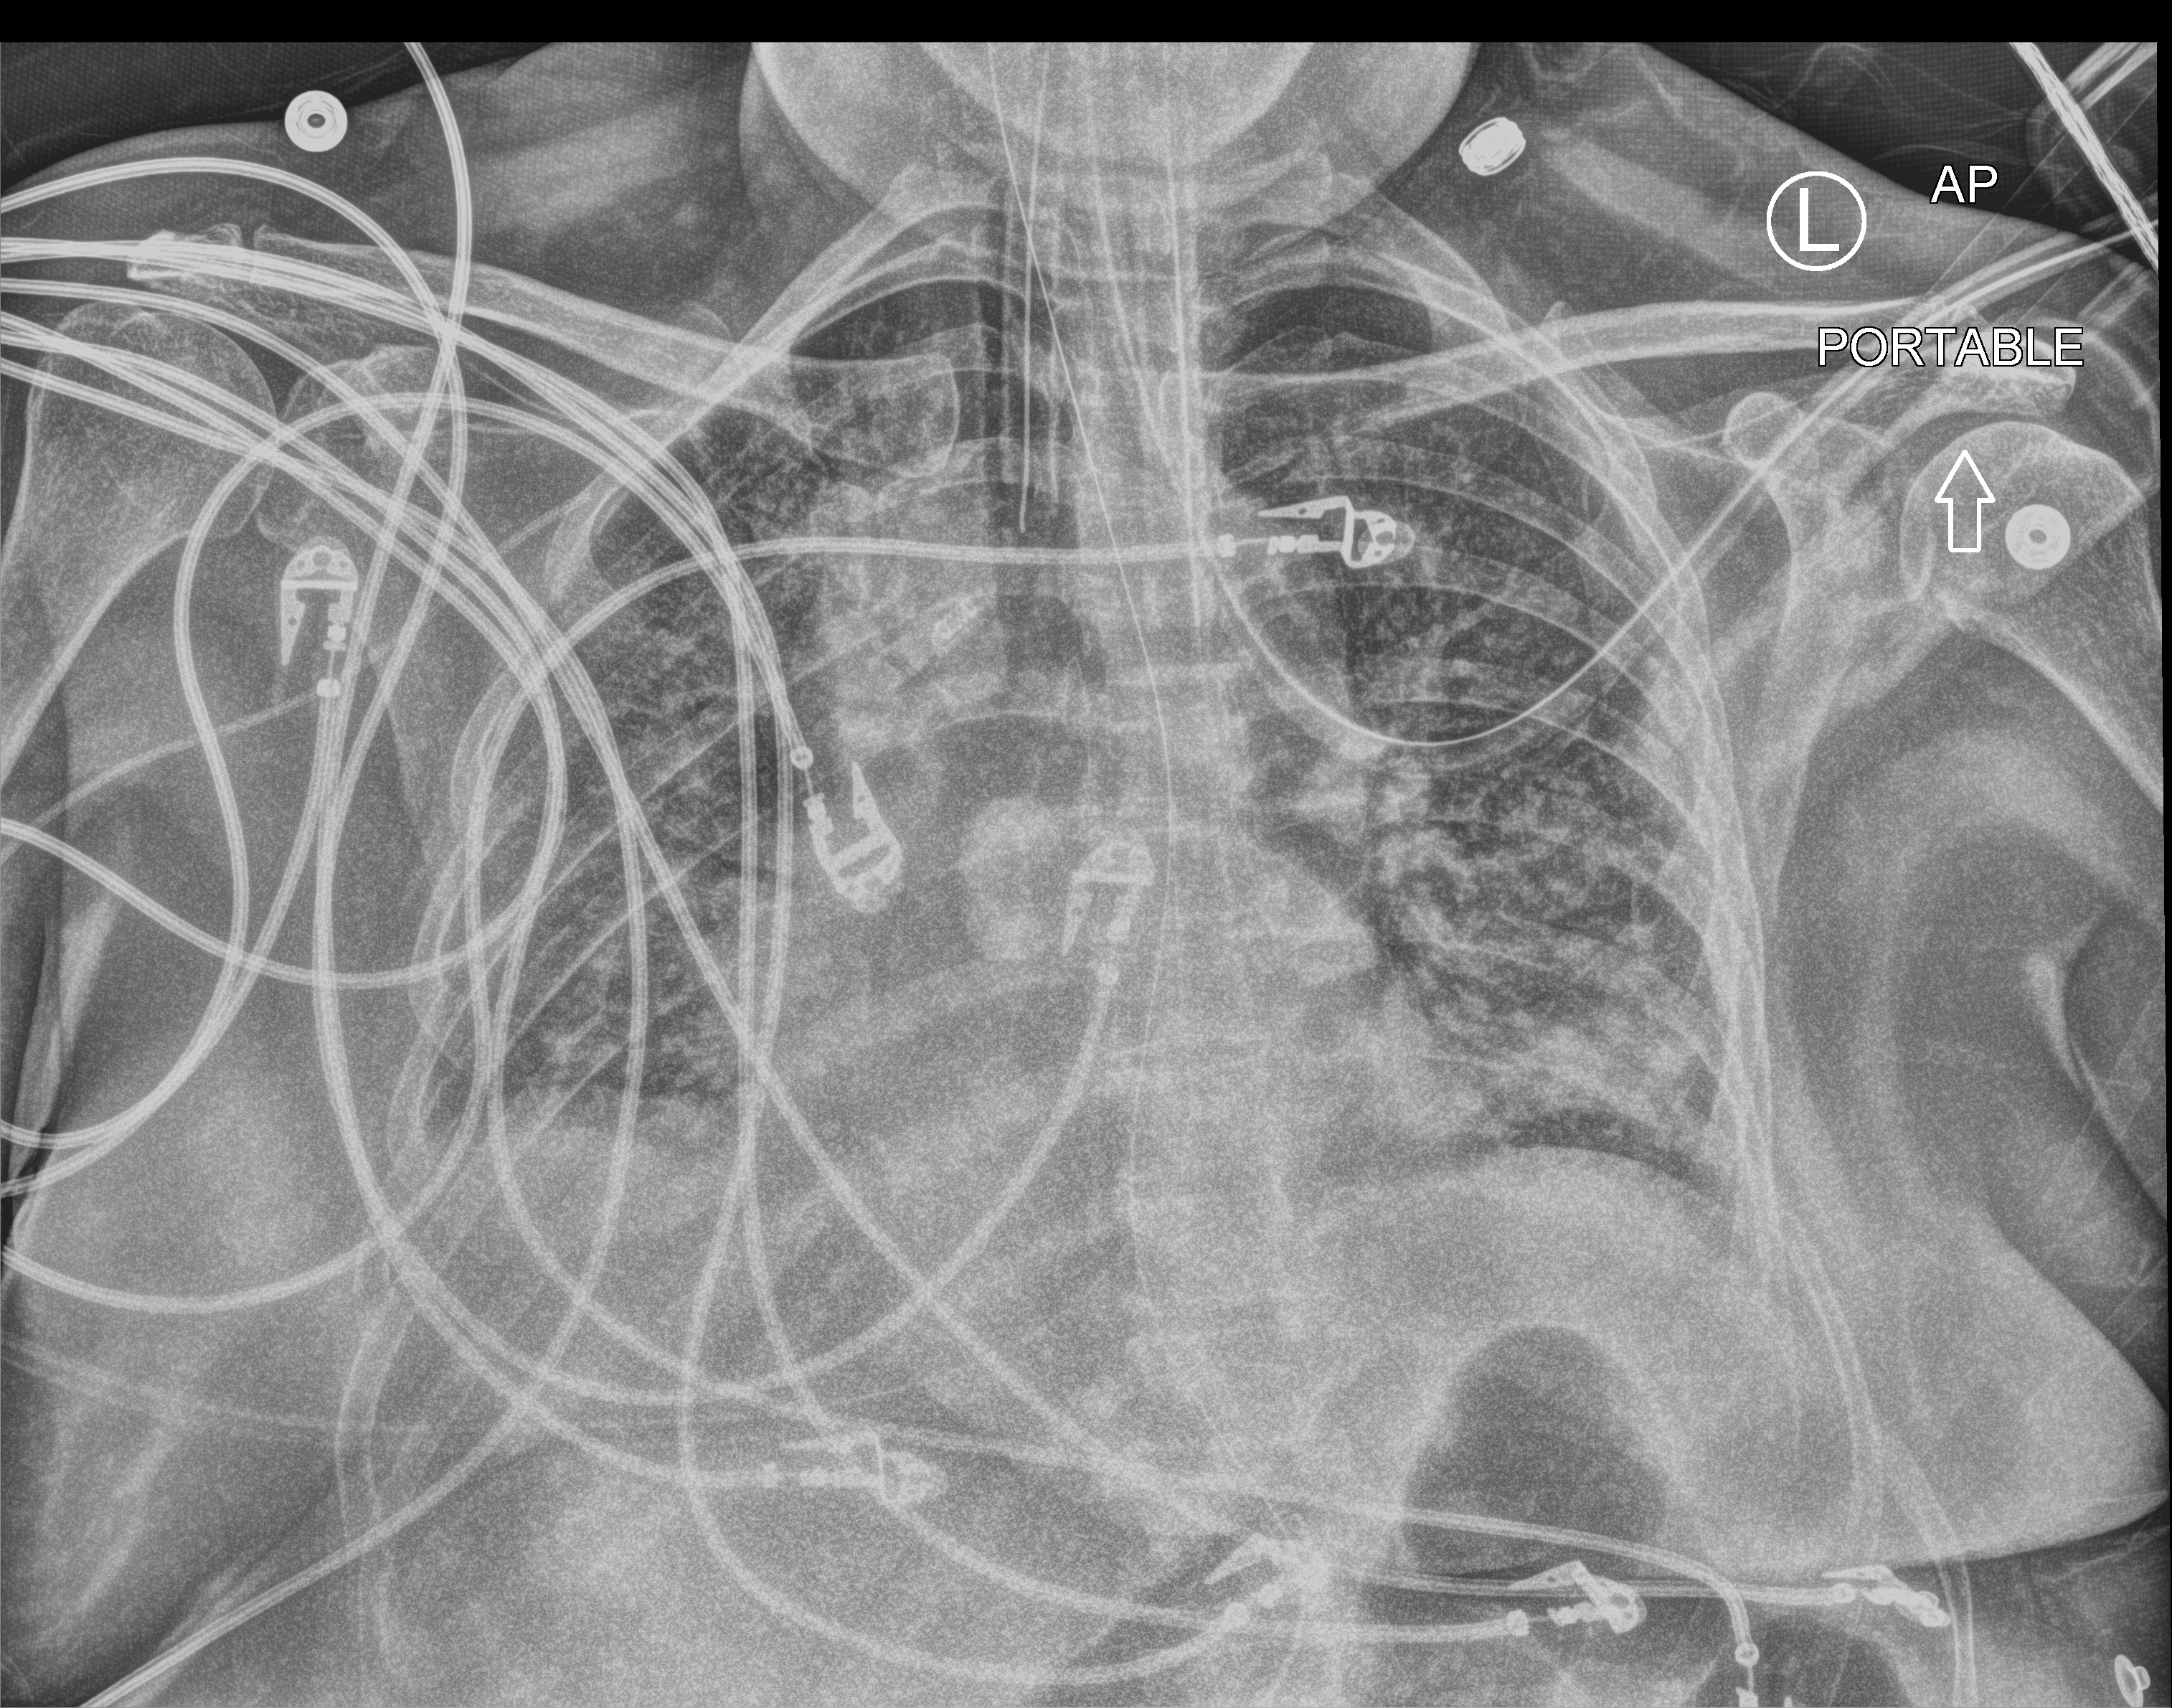
Portable chest radiograph, anteroposterior (AP) projection. Female patient hospitalised with COVID-19, age 18–59 years.
Admission-level facts for this patient (not findings on this image; timing relative to this image not recorded): admitted to intensive care during this hospital stay: yes; mechanically ventilated during this hospital stay: yes.